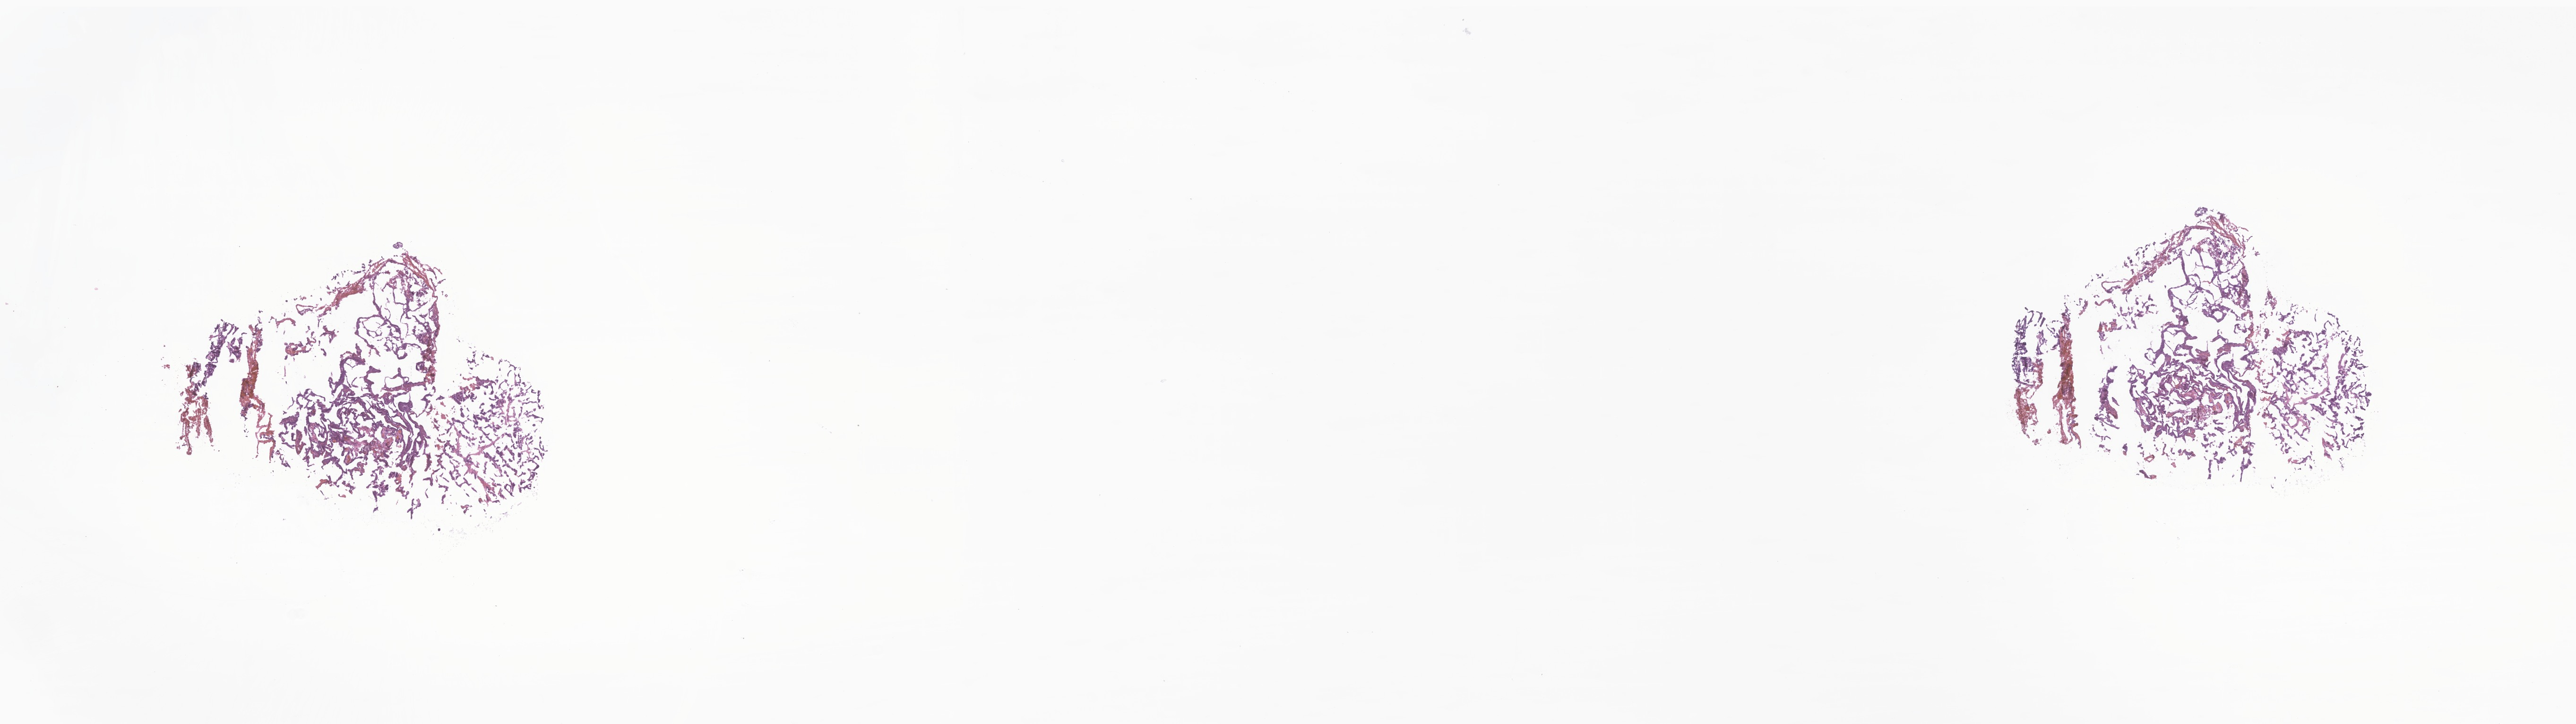
Digitized haematoxylin and eosin-stained section of tumor tissue from the brain — shown as a low-resolution overview of the whole scanned area (about 23.0 x 6.5 mm). Frozen section. Male patient, age 91 months (7 years 7 months).
Recorded diagnosis: Medulloblastoma, NOS.